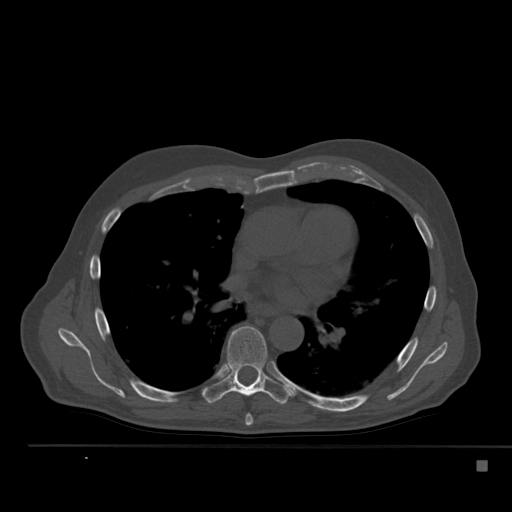
CT including the spine, one axial slice. Slice 331 of 517 in the series (ordered by position). Reconstruction kernel Br40s. 120 kVp. Bone window (W 1800 / L 400 HU). 1.5 mm slice thickness. 512 × 512 image matrix. Male patient, age 70 years. Case-level facts recorded for this patient, not image findings: primary cancer: renal; vertebrae with lytic lesions (as recorded): T4, T6, T10, T12, L3, L4, L5.
Structures marked on this image (semi-automatically segmented with operator editing):
- T6 vertebra: bounding box [x1, y1, x2, y2] px = [245, 414, 253, 426]
- T7 vertebra: [201, 326, 291, 405]